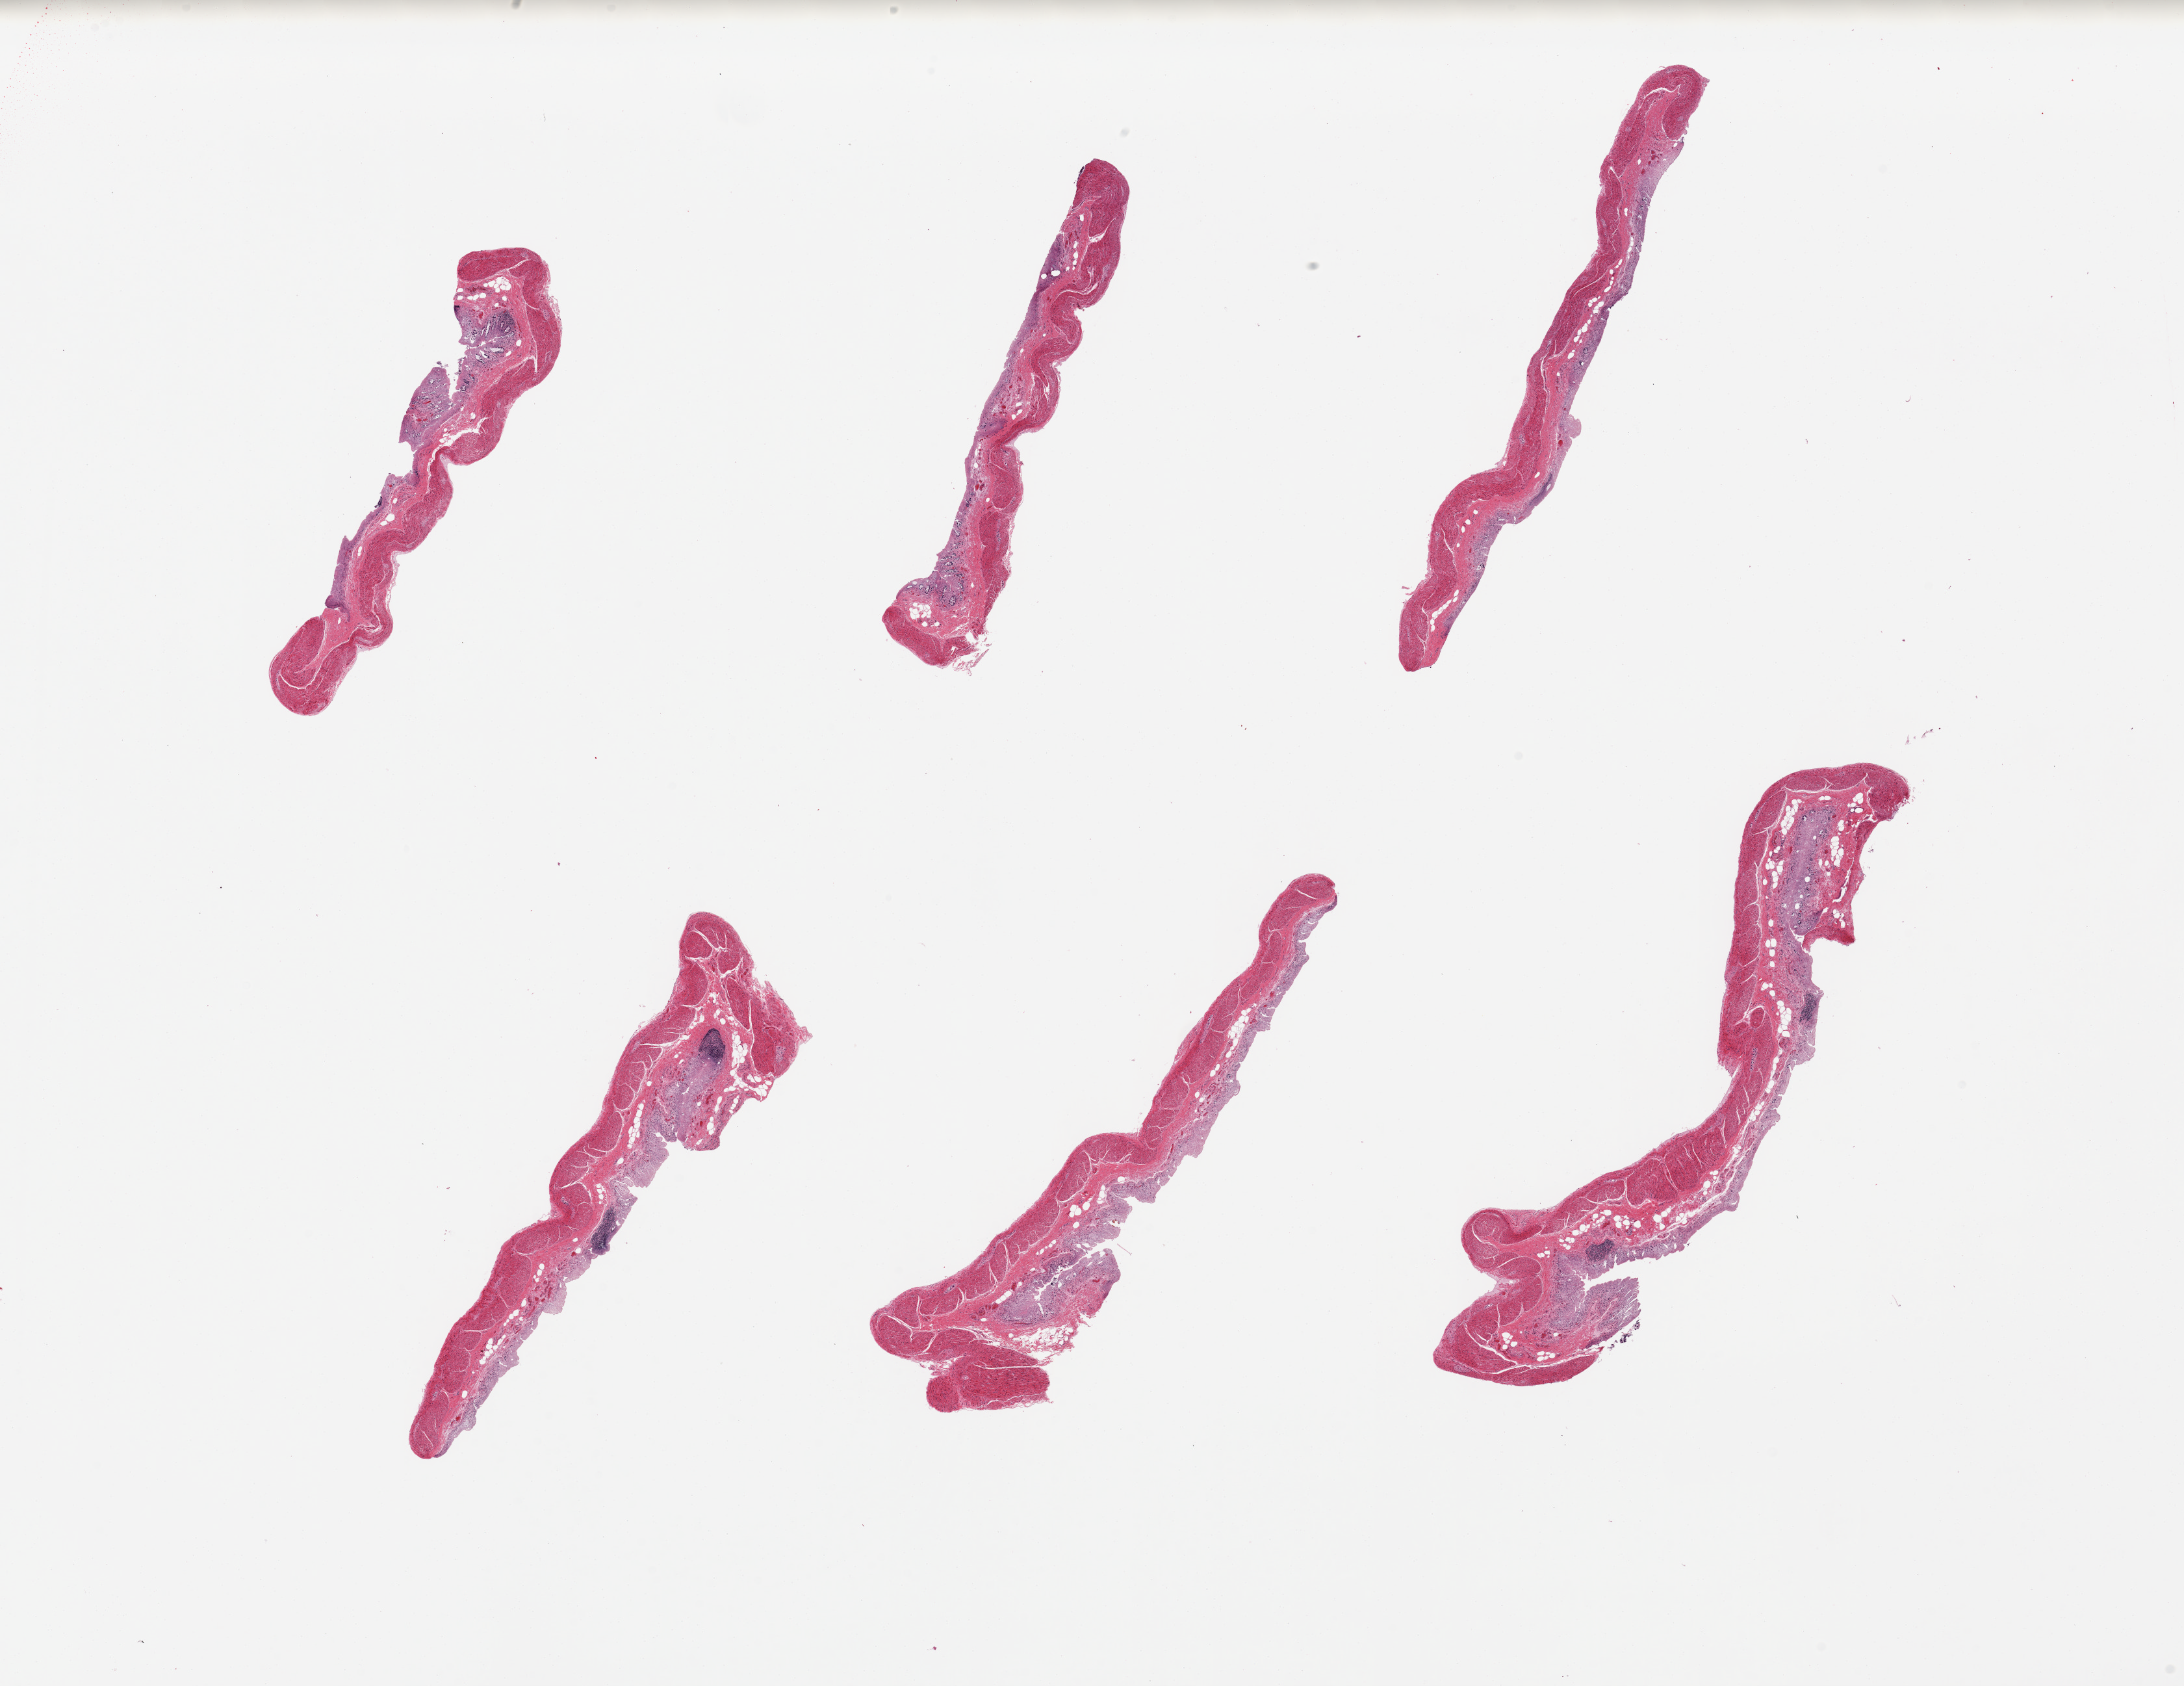
Digitized H&E-stained section, a low-resolution overview of the entire scanned area, about 26.6 x 20.5 mm (acquisition: 20x scan), PAXgene-fixed paraffin-embedded (PFPE) section, target tissue: transverse colon, donor tissue sample. Donor sex: female.
Pathologist's review note for this sample: 6 pieces; mucosa ~10-40% thickness but totally autolyzed/sloughing.